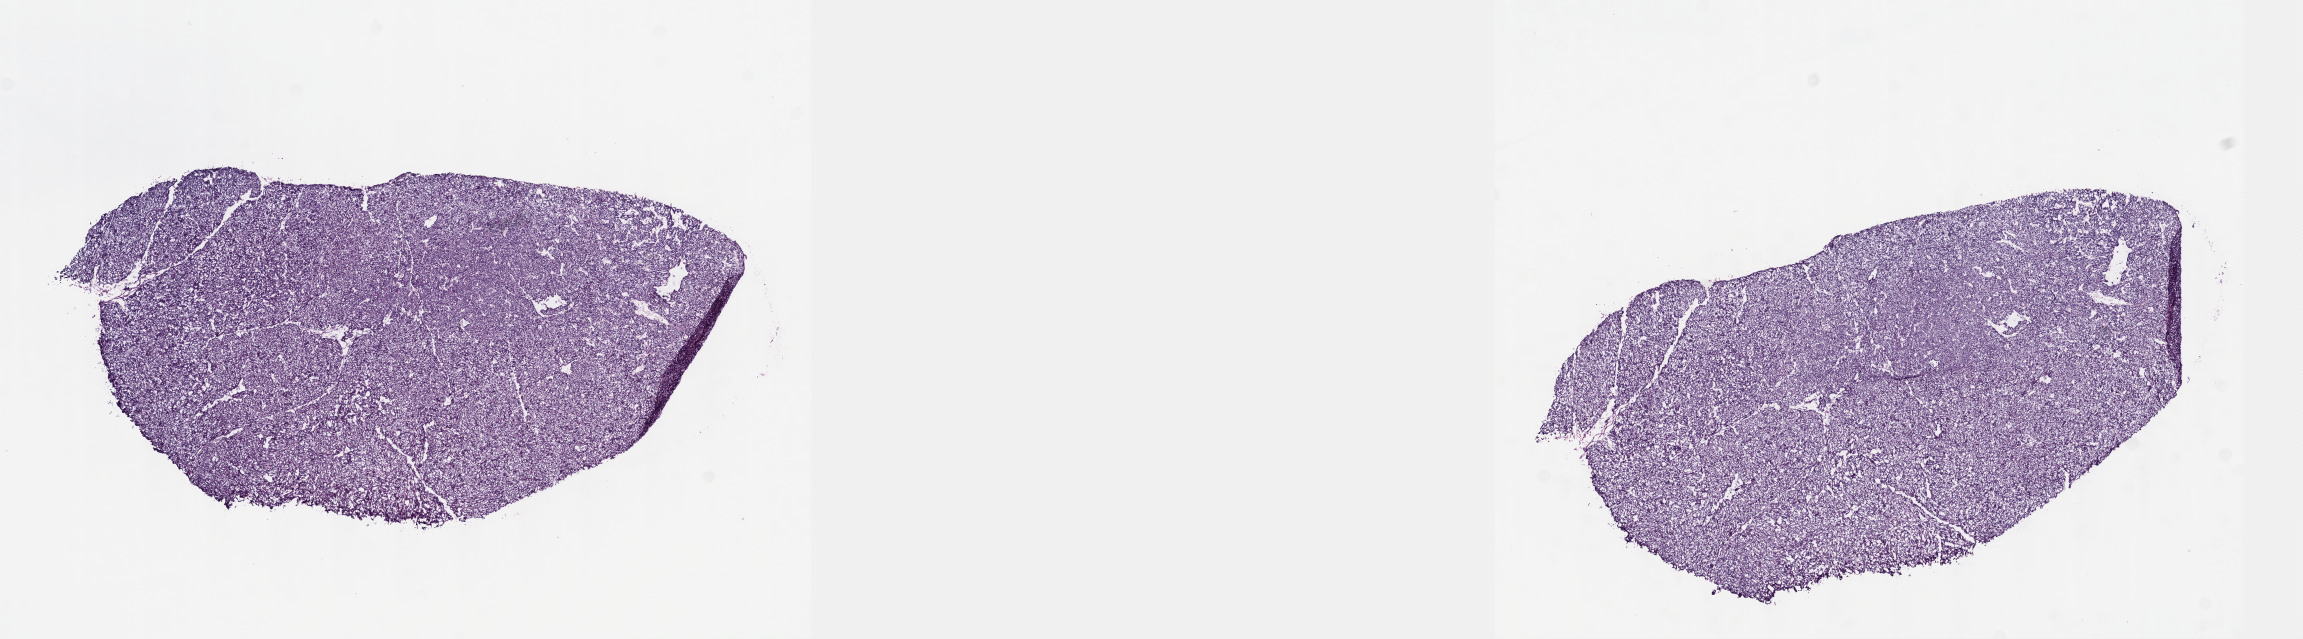
H&E-stained whole-slide image, low-resolution overview of the scanned area, about 18.6 x 5.2 mm (from a 40x scan), frozen section from the top of the tissue portion, thymus, primary tumour sample. Patient: male, age at initial diagnosis 70 years. Slide review estimates, as recorded: tumour cells 99%, tumour nuclei 99%, normal cells 0%, stromal cells 1%, necrosis 0%. Infiltration values recorded for this section: lymphocyte infiltration 0%, monocyte infiltration 0%, neutrophil infiltration 0%.
* diagnosis: Thymoma, type A, malignant (anterior mediastinum)